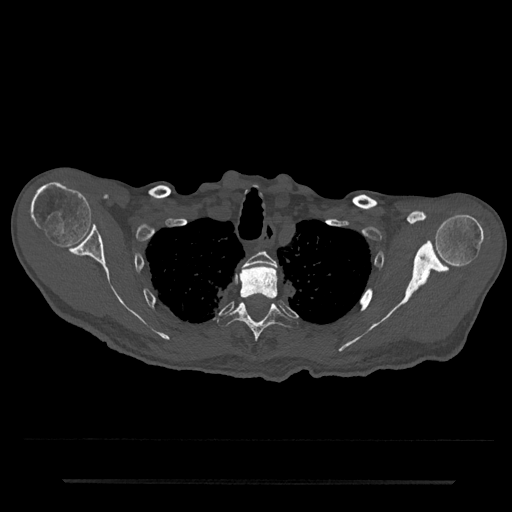
CT including the spine, one axial slice. Position 644 of 797 along the scan axis. 120 kVp. Bone window (W 1800 / L 400 HU). 512 × 512 image matrix, field of view 427 × 427 mm. Male patient, age 74 years. Case-level facts recorded for this patient, not image findings: primary cancer: prostate.
Annotated regions visible in this slice (semi-automatically segmented with operator editing):
- T2 vertebra: bounding box (x1, y1, x2, y2) in pixels: (242, 251, 277, 268)
- T3 vertebra: (239, 265, 278, 299)
- T4 vertebra: (217, 302, 298, 341)